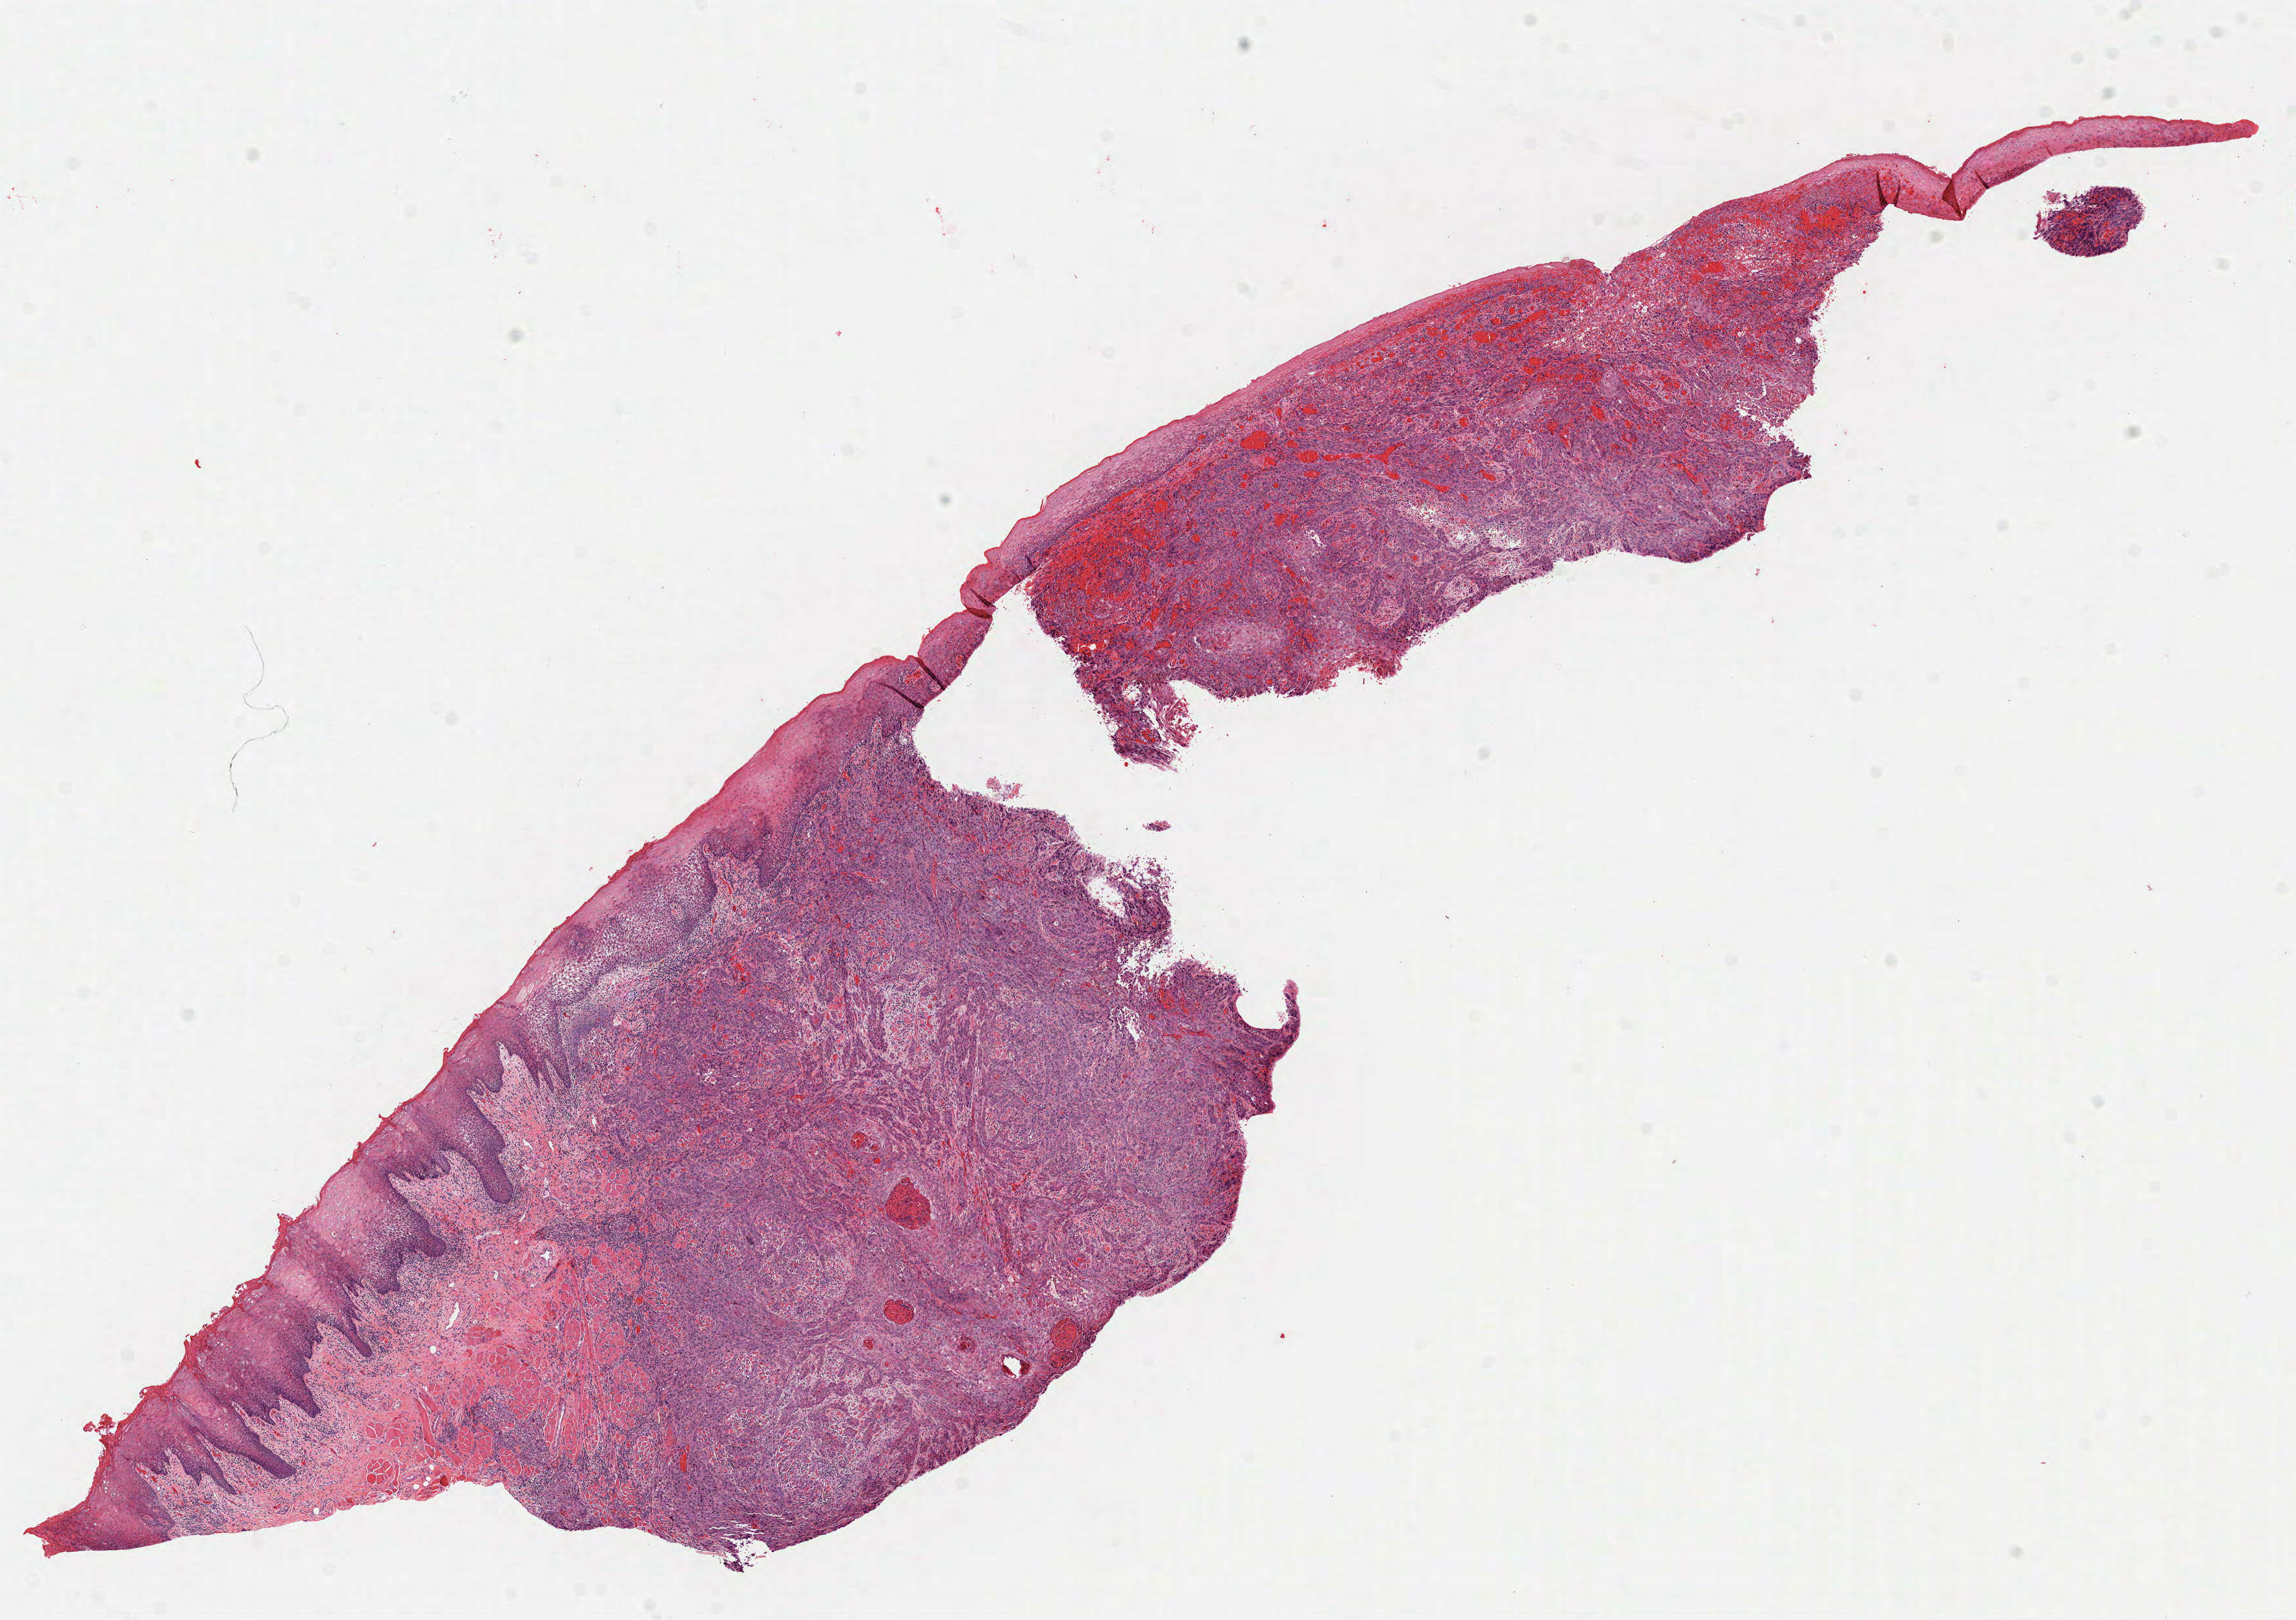
Whole-slide histology image, Hematoxylin and eosin (H&E) stained, shown as a low-resolution overview of the whole scanned area (about 14.3 x 10.1 mm, from a 40x scan), formalin-fixed paraffin-embedded (FFPE) diagnostic section, sample: primary tumour, head and neck. Patient: male, age at initial diagnosis 28 years. Histologic grade: G2 (moderately differentiated).
Histologic diagnosis: Squamous cell carcinoma, NOS (tongue, NOS). TNM: T4a N2b. AJCC pathologic stage: IVA (7th edition). Laterality: left.